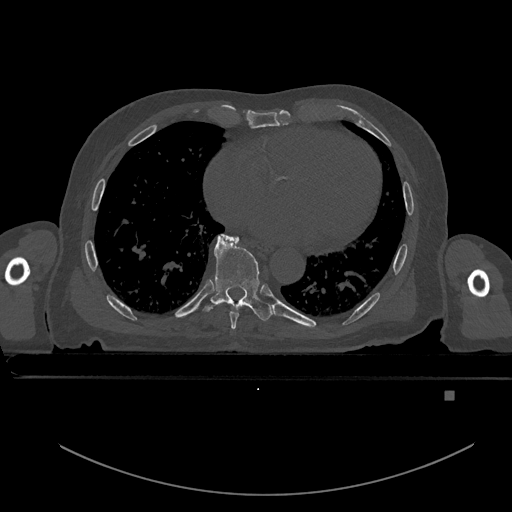
CT including the spine, one axial slice. Slice 217 of 969 in the series (ordered by position). Bone window (W 1800 / L 400 HU). 0.5 mm slice thickness. 512 × 512 image matrix, field of view 456 × 456 mm. Patient: male, 82 years. Case-level facts recorded for this patient, not image findings: primary cancer: prostate.
Structures marked on this image (semi-automatic segmentation, software-assisted and operator-edited):
- T7 vertebra: bounding box <225,235,239,328> (left, top, right, bottom; pixels)
- T8 vertebra: <204,235,273,321>